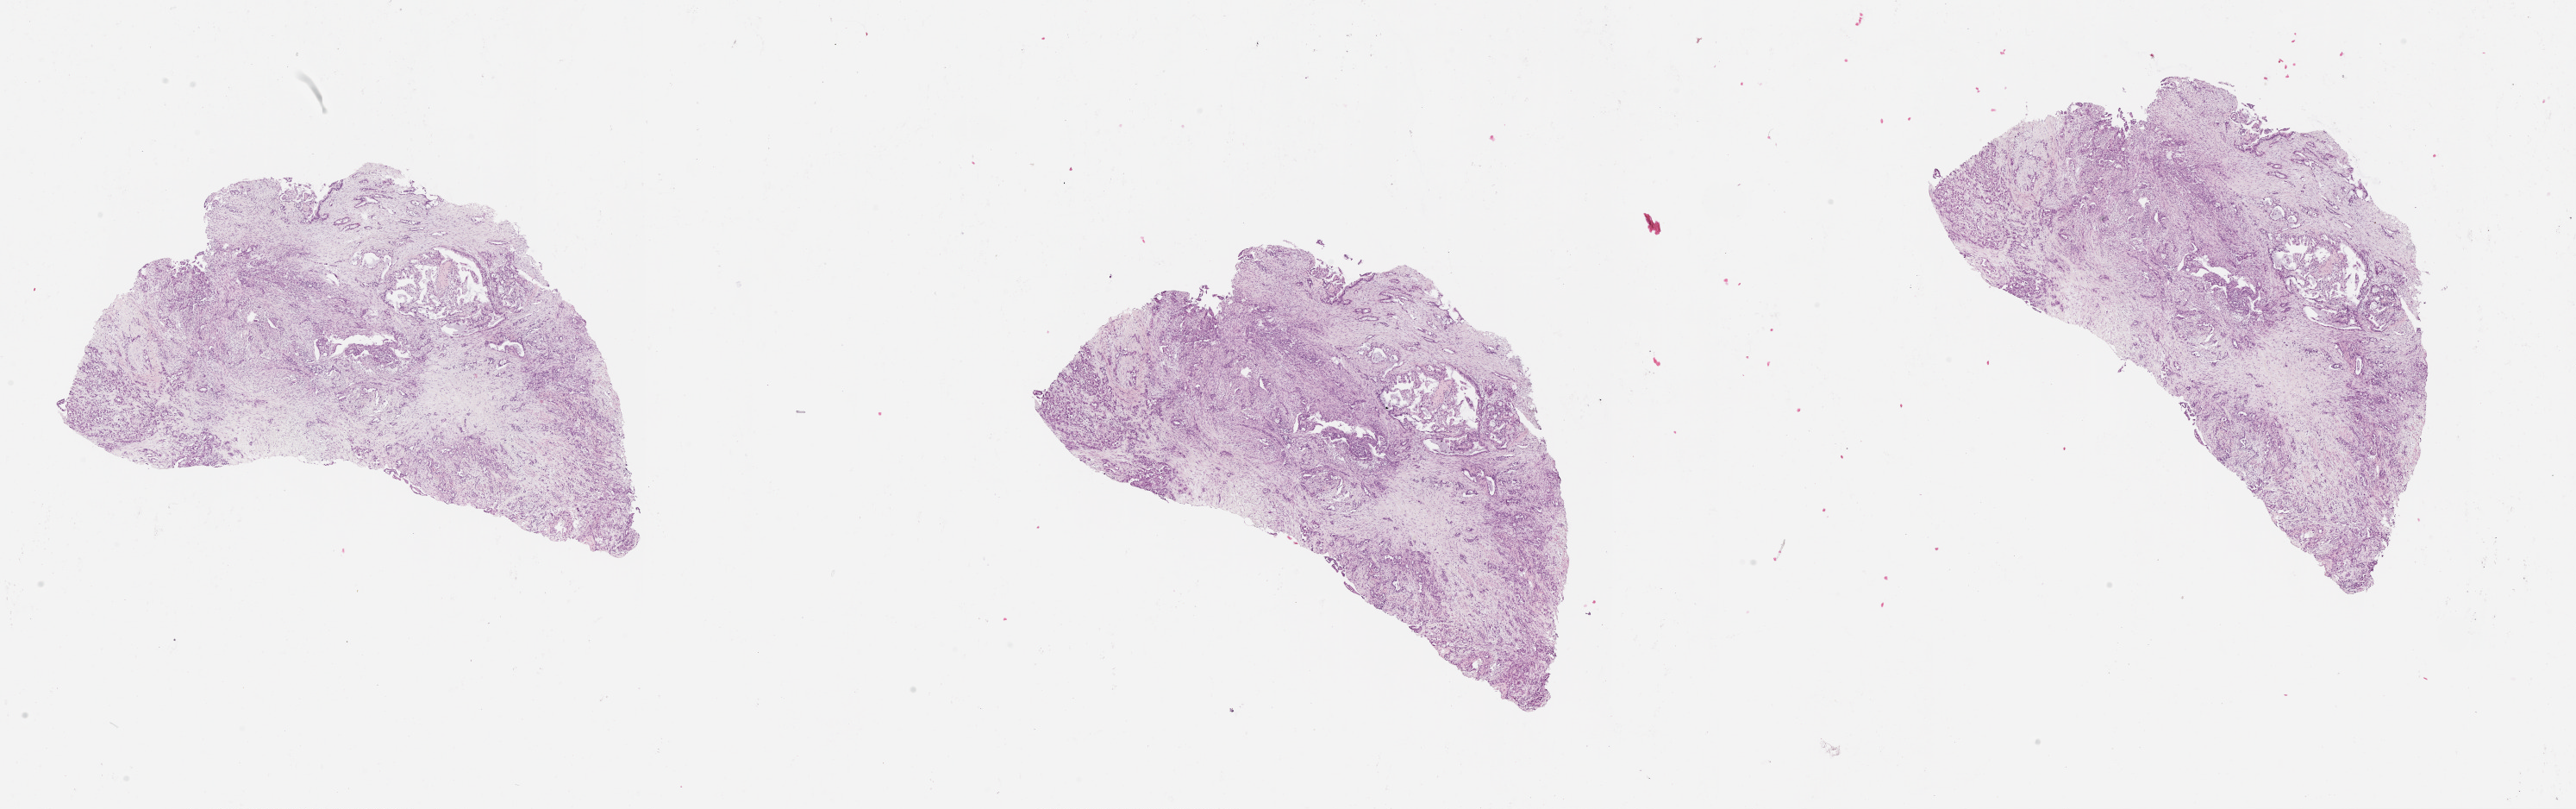
Digitized H&E-stained tissue section (whole slide), whole scanned area (about 24.1 x 7.6 mm, acquisition: 20x scan) shown as a low-resolution overview; tumour tissue sample, sampled site: pancreas. Male, 75 y/o. Histologic grade: G3 (poorly differentiated). Pathologist review of this section (percent, as recorded): tumour nuclei 50%, necrosis 0%.
Diagnosis: Infiltrating duct carcinoma, NOS. Primary tumour site (as recorded): head. AJCC pathologic stage: IV.